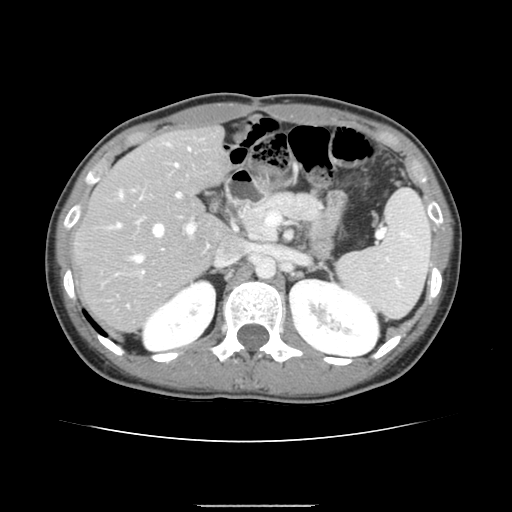
Contrast-enhanced abdominal CT, one axial slice. Slice 89 of 150 in the series (ordered by position). 120 kVp. Soft-tissue window (W 400 / L 40 HU). 2.5 mm slice thickness. 512 × 512 image matrix, field of view 324 × 324 mm. Female patient, age 32 years. From the clinical record (not read from this slice): diagnosis: colorectal cancer liver metastases, imaged before liver resection.
Annotated regions visible in this slice (expert manual segmentation):
- hepatic veins: bounding box <117,148,190,262> (left, top, right, bottom; pixels)
- liver: <77,128,227,332>
- planned liver remnant (the part of the liver to remain after resection): <77,128,226,276>
- portal vein (with intrahepatic branches): <109,190,195,275>